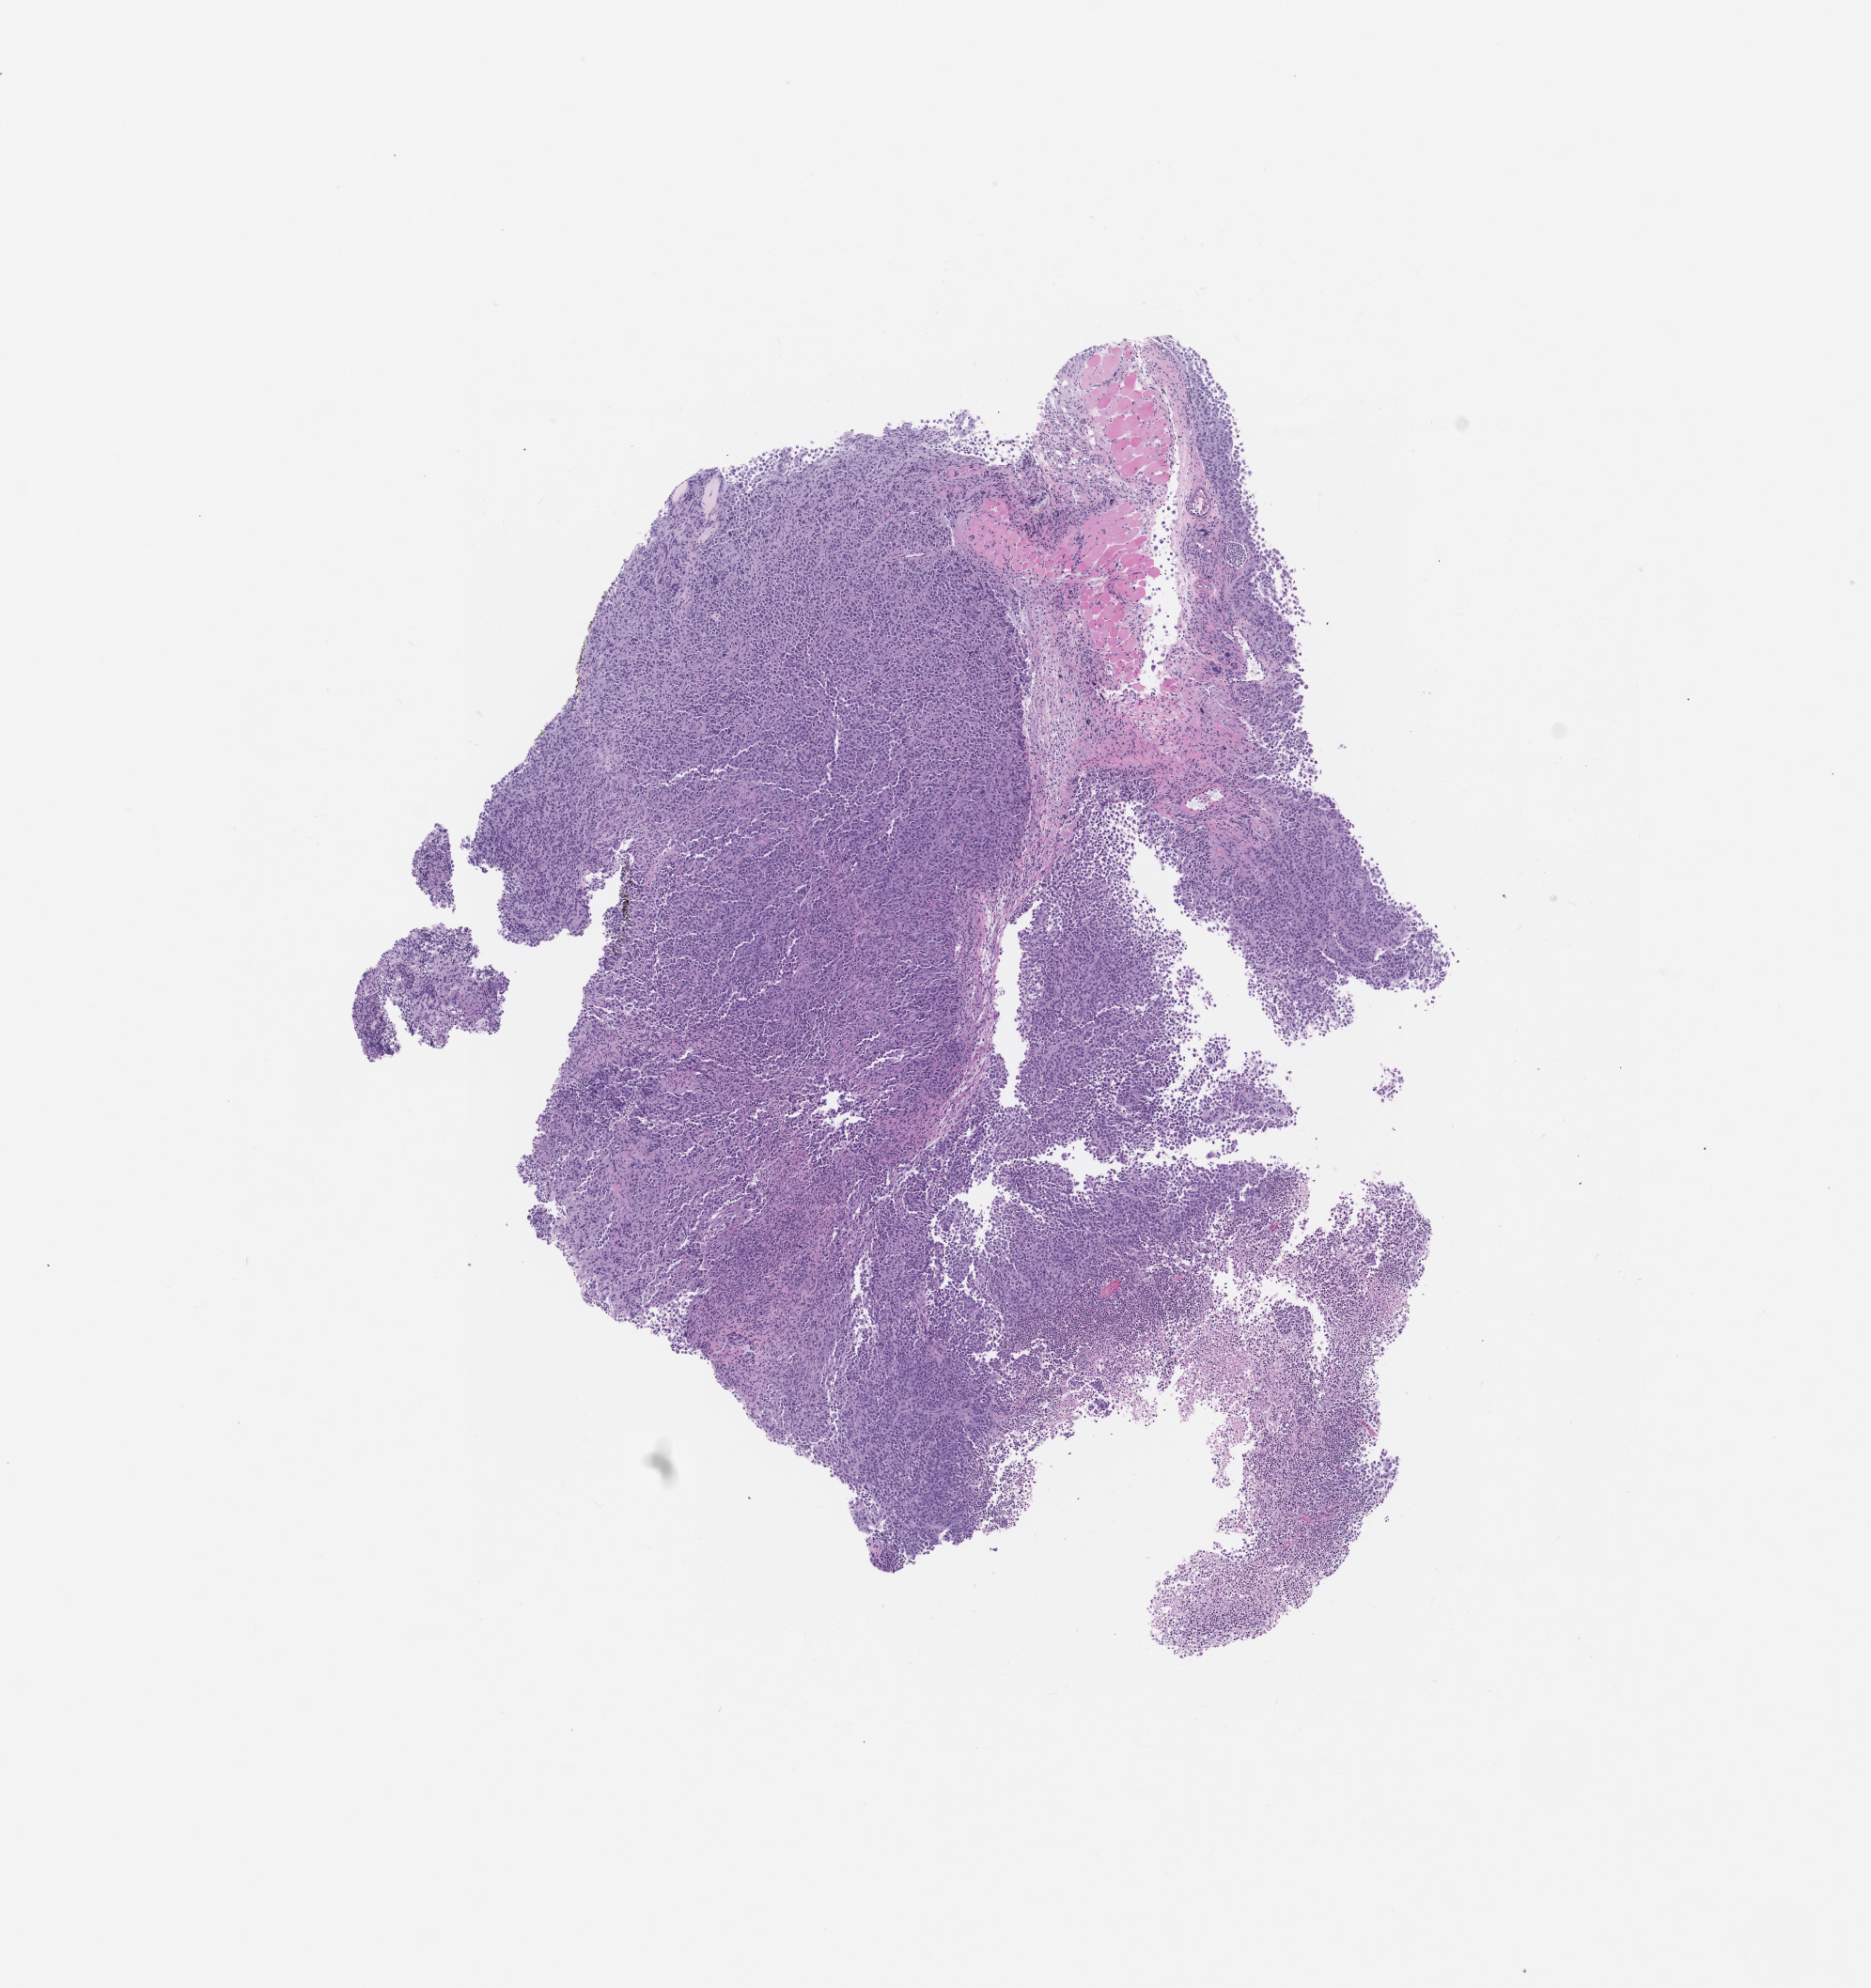
Whole-slide image, H&E: patient-derived xenograft (human tumor grown in a mouse), passage 0, shown as a low-resolution overview of the whole scanned area (about 8.0 x 8.5 mm), formalin-fixed paraffin-embedded section, originating tumor site category: skin.
Originating patient diagnosis: Melanoma.